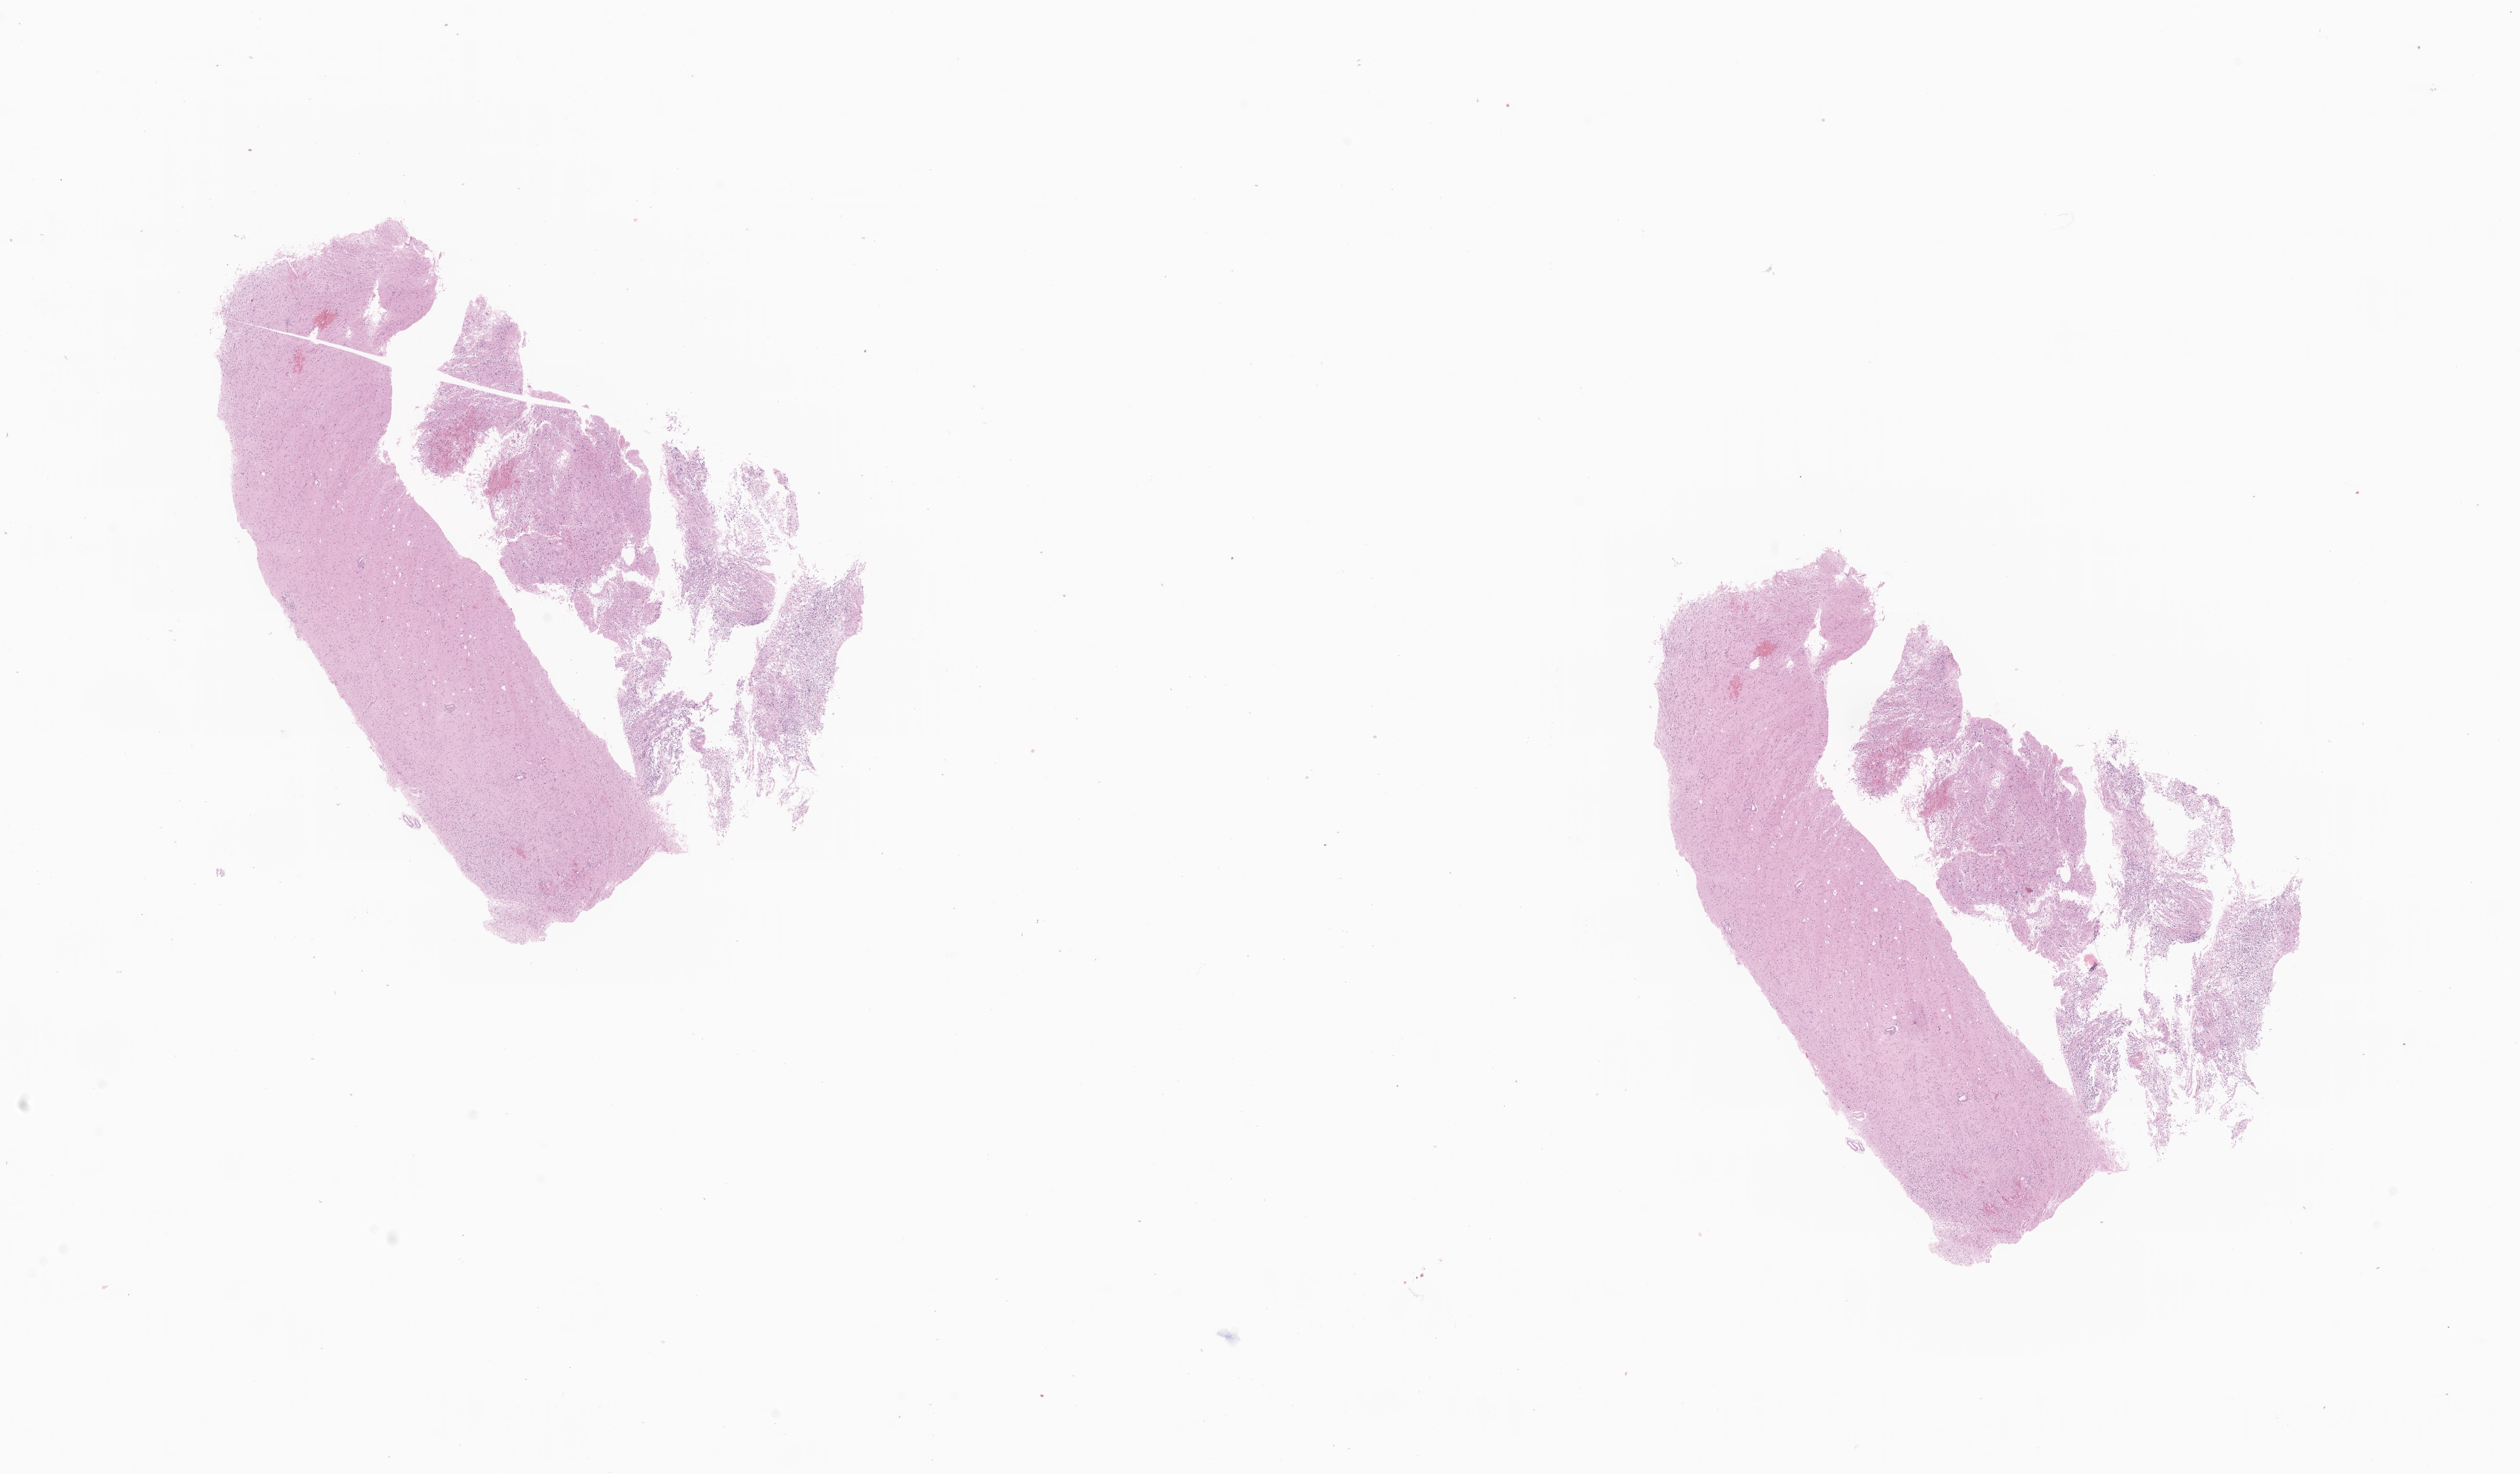
Whole-slide image, haematoxylin and eosin stain of tumor tissue from the brain — shown as a low-resolution overview of the whole scanned area (about 21.7 x 12.7 mm). FFPE section. Male patient, age 93 months (7 years 9 months).
Diagnosis: Neoplasm, malignant.